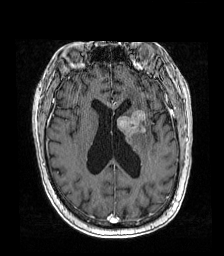
Brain MRI from a brain-tumour surgery series, one axial slice; slice 73 of 192 in the series (ordered by position); T1-weighted post-contrast; 224 × 256 image matrix, field of view 219 × 250 mm. Case-level facts recorded for this patient, not image findings: histopathology: Metastatic carcinoma from lung primary; tumour location: Left Frontal Caudate.
Structures marked on this image (expert manual segmentation):
- tumour: box from (x=117, y=110) to (x=148, y=145) px